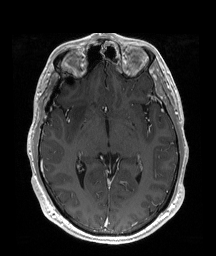
Brain MRI from a brain-tumour surgery series, one axial slice. Position 109 of 192 along the scan axis. T1-weighted post-contrast. 1 mm slice thickness. 216 × 256 image matrix, field of view 219 × 260 mm. Case-level facts recorded for this patient, not image findings: histopathology: Astrocytoma; WHO grade: 2.
Outlined on this slice (manually delineated by an expert):
- tumour: bounding box [x1, y1, x2, y2] px = [69, 95, 91, 133]